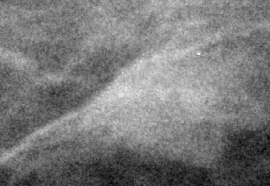
Region of interest cut from a scanned film mammogram (one marked finding), right breast, MLO view.
Finding: mass, shape irregular, margins ill defined; BI-RADS assessment category 4; pathology result (as recorded, not read from the image): malignant.